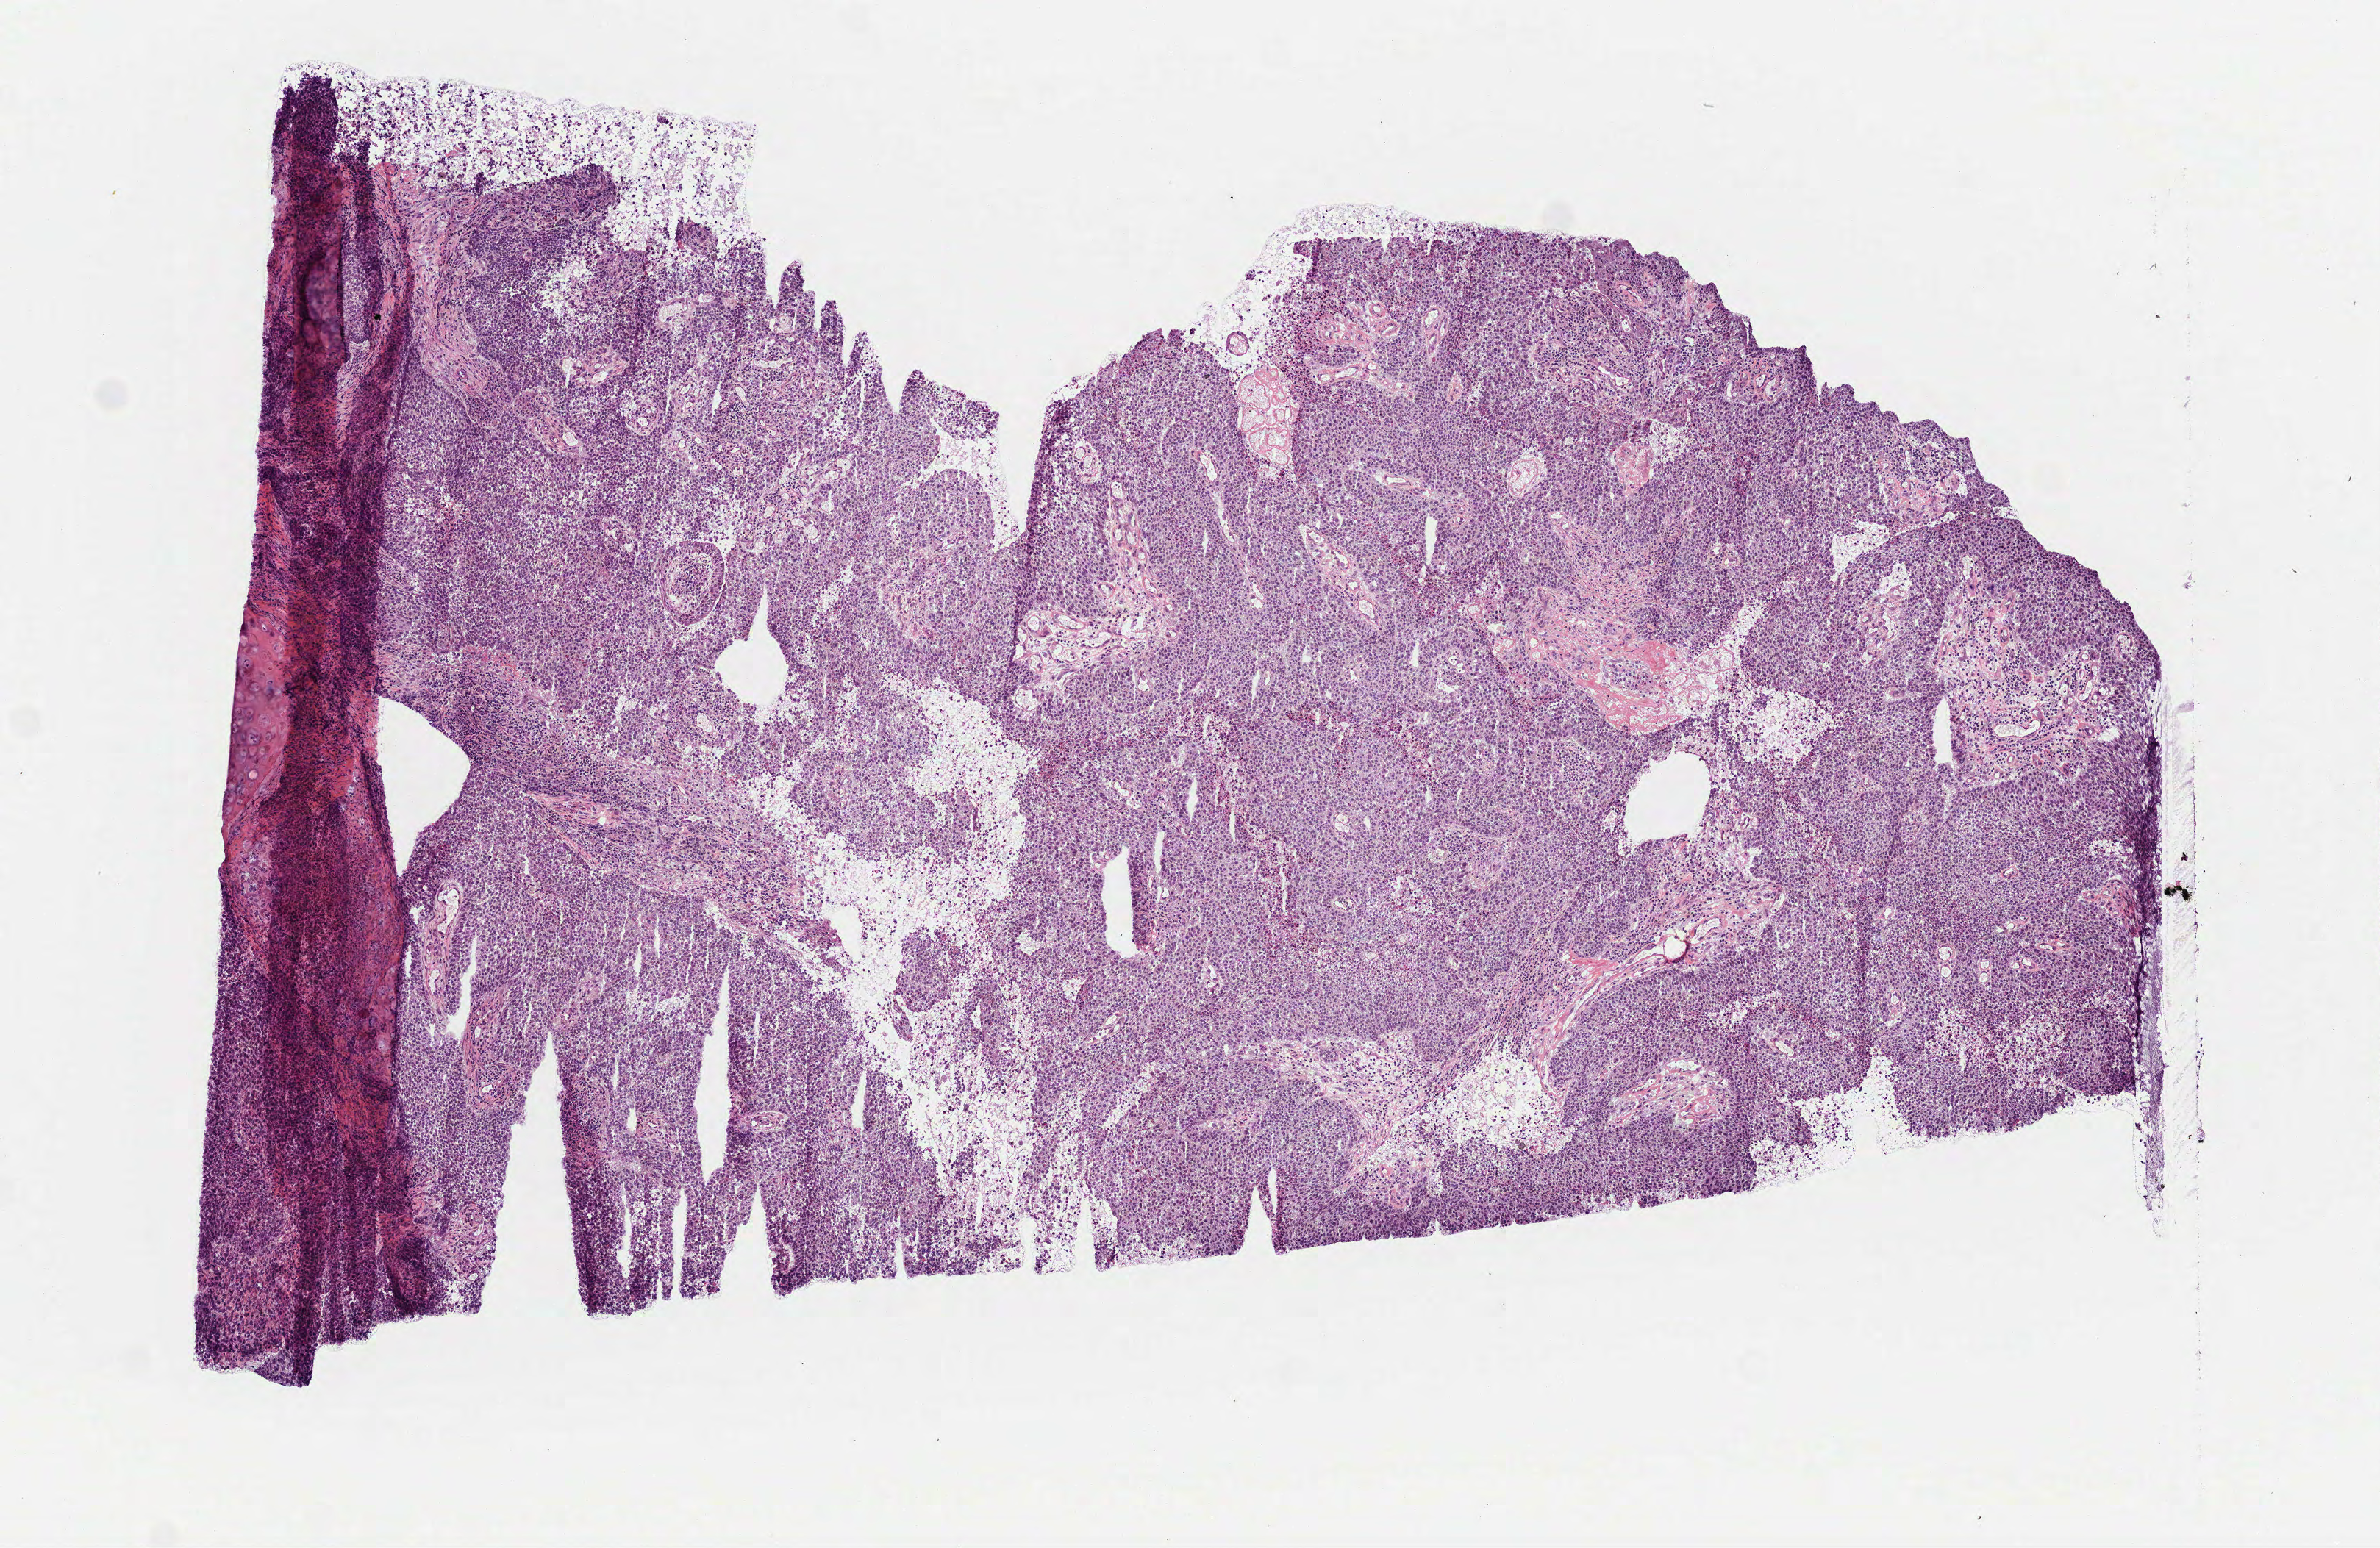
Whole-slide histology image, H&E-stained, whole scanned area (about 6.5 x 4.2 mm) shown as a low-resolution overview; frozen section from the top of the tissue portion; sample: primary tumour, lung. Male patient. Slide review estimates, as recorded: tumour cells 98%, tumour nuclei 83%, normal cells 0%, stromal cells 0%, necrosis 2%. Infiltration values recorded for this section: lymphocyte infiltration 5%, monocyte infiltration 1%, neutrophil infiltration 2%.
Laterality: left. Pathologic diagnosis: Squamous cell carcinoma, NOS (lower lobe, lung). AJCC pathologic stage: IIA (6th edition).